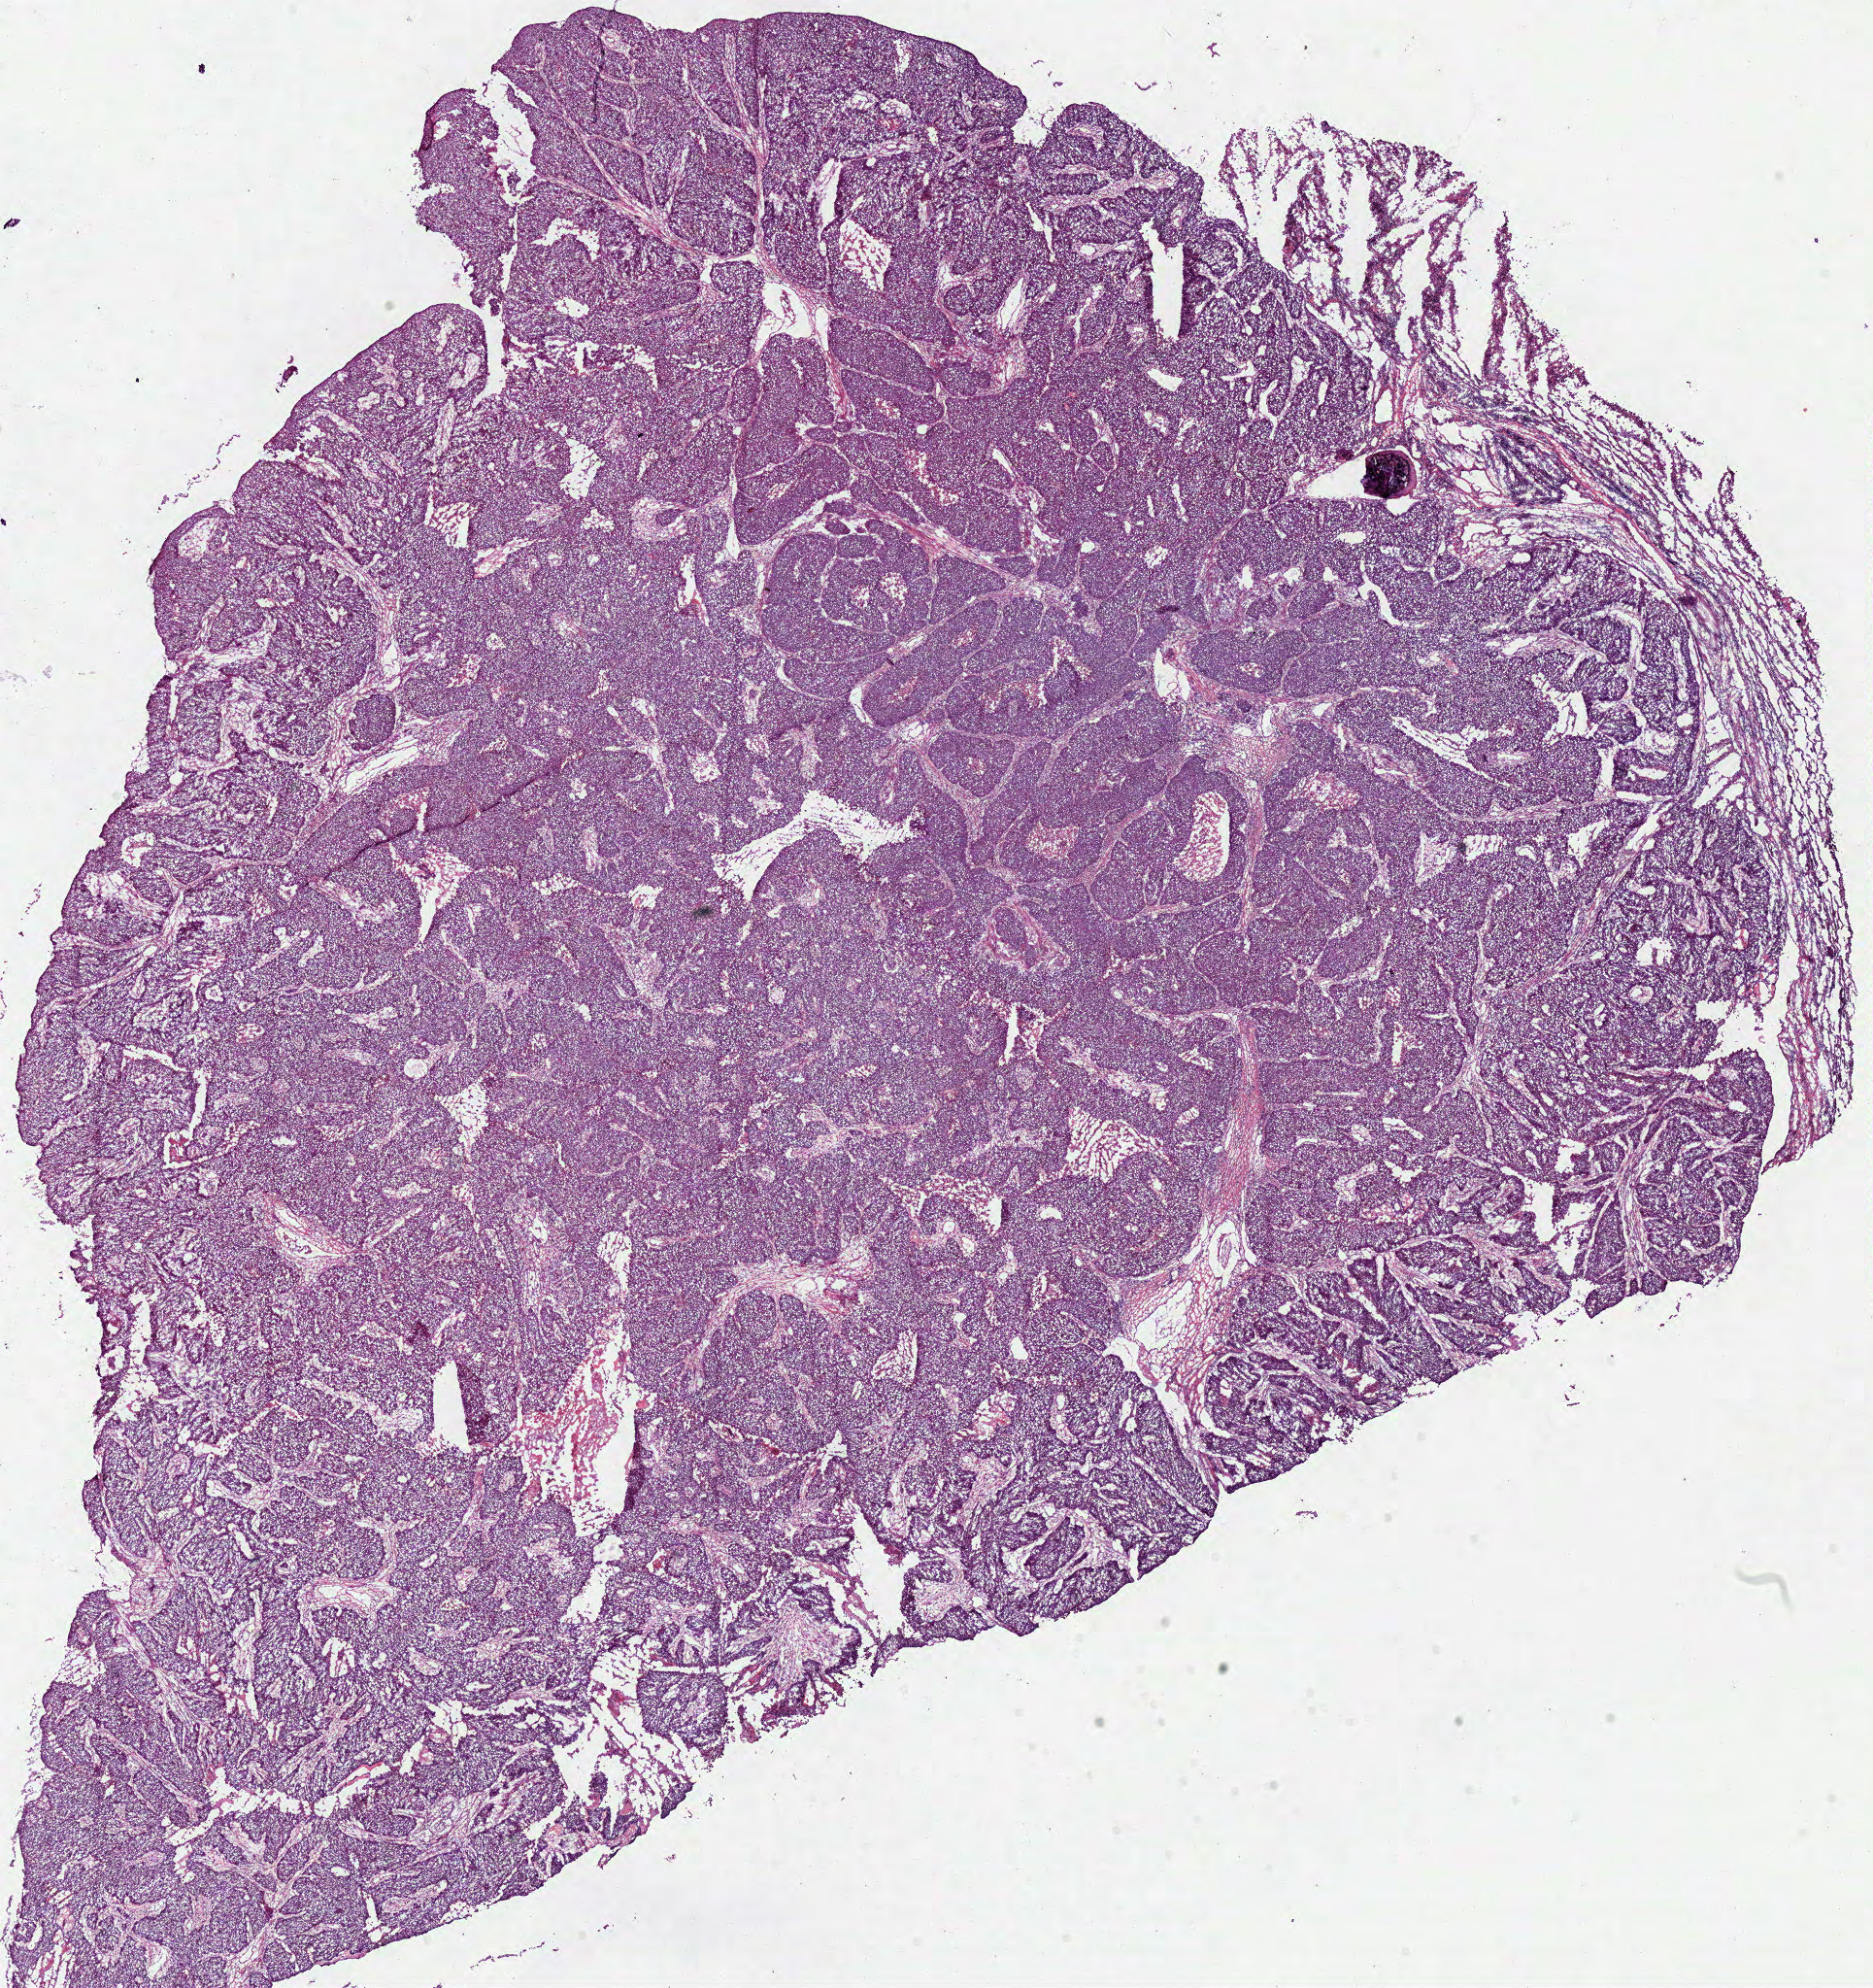
Digitized H&E tissue section (whole slide), whole scanned area (about 15.2 x 16.1 mm) shown as a low-resolution overview, frozen section from the bottom of the tissue portion, sample: primary tumour, lung. Male patient; age at initial diagnosis 65 years. Slide review estimates, as recorded: tumour cells 82%, tumour nuclei 85%.
Pathologic diagnosis: Papillary squamous cell carcinoma (upper lobe, lung).